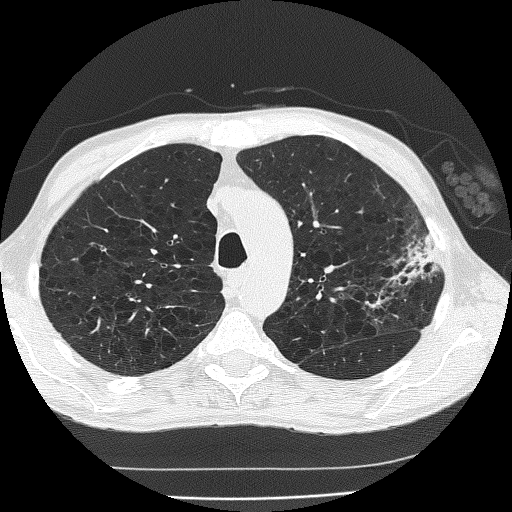
Chest CT (low-dose screening protocol), one axial image, second annual screen, lung window (W 1500 / L -600 HU), 120 kVp. Male, age 60 years at enrolment. Current smoker at enrolment.
Expert-annotated lung lesion, box from (x=346, y=234) to (x=446, y=335) px. The screening reader recorded 2 non-calcified nodules or masses ≥4 mm on this exam; which of them this box marks is not recorded. Official screen result: positive, other. Lung cancer was diagnosed 178 days after this screen: bronchiolo-alveolar carcinoma, mucinous, left upper lobe, stage IV (AJCC 6th edition).